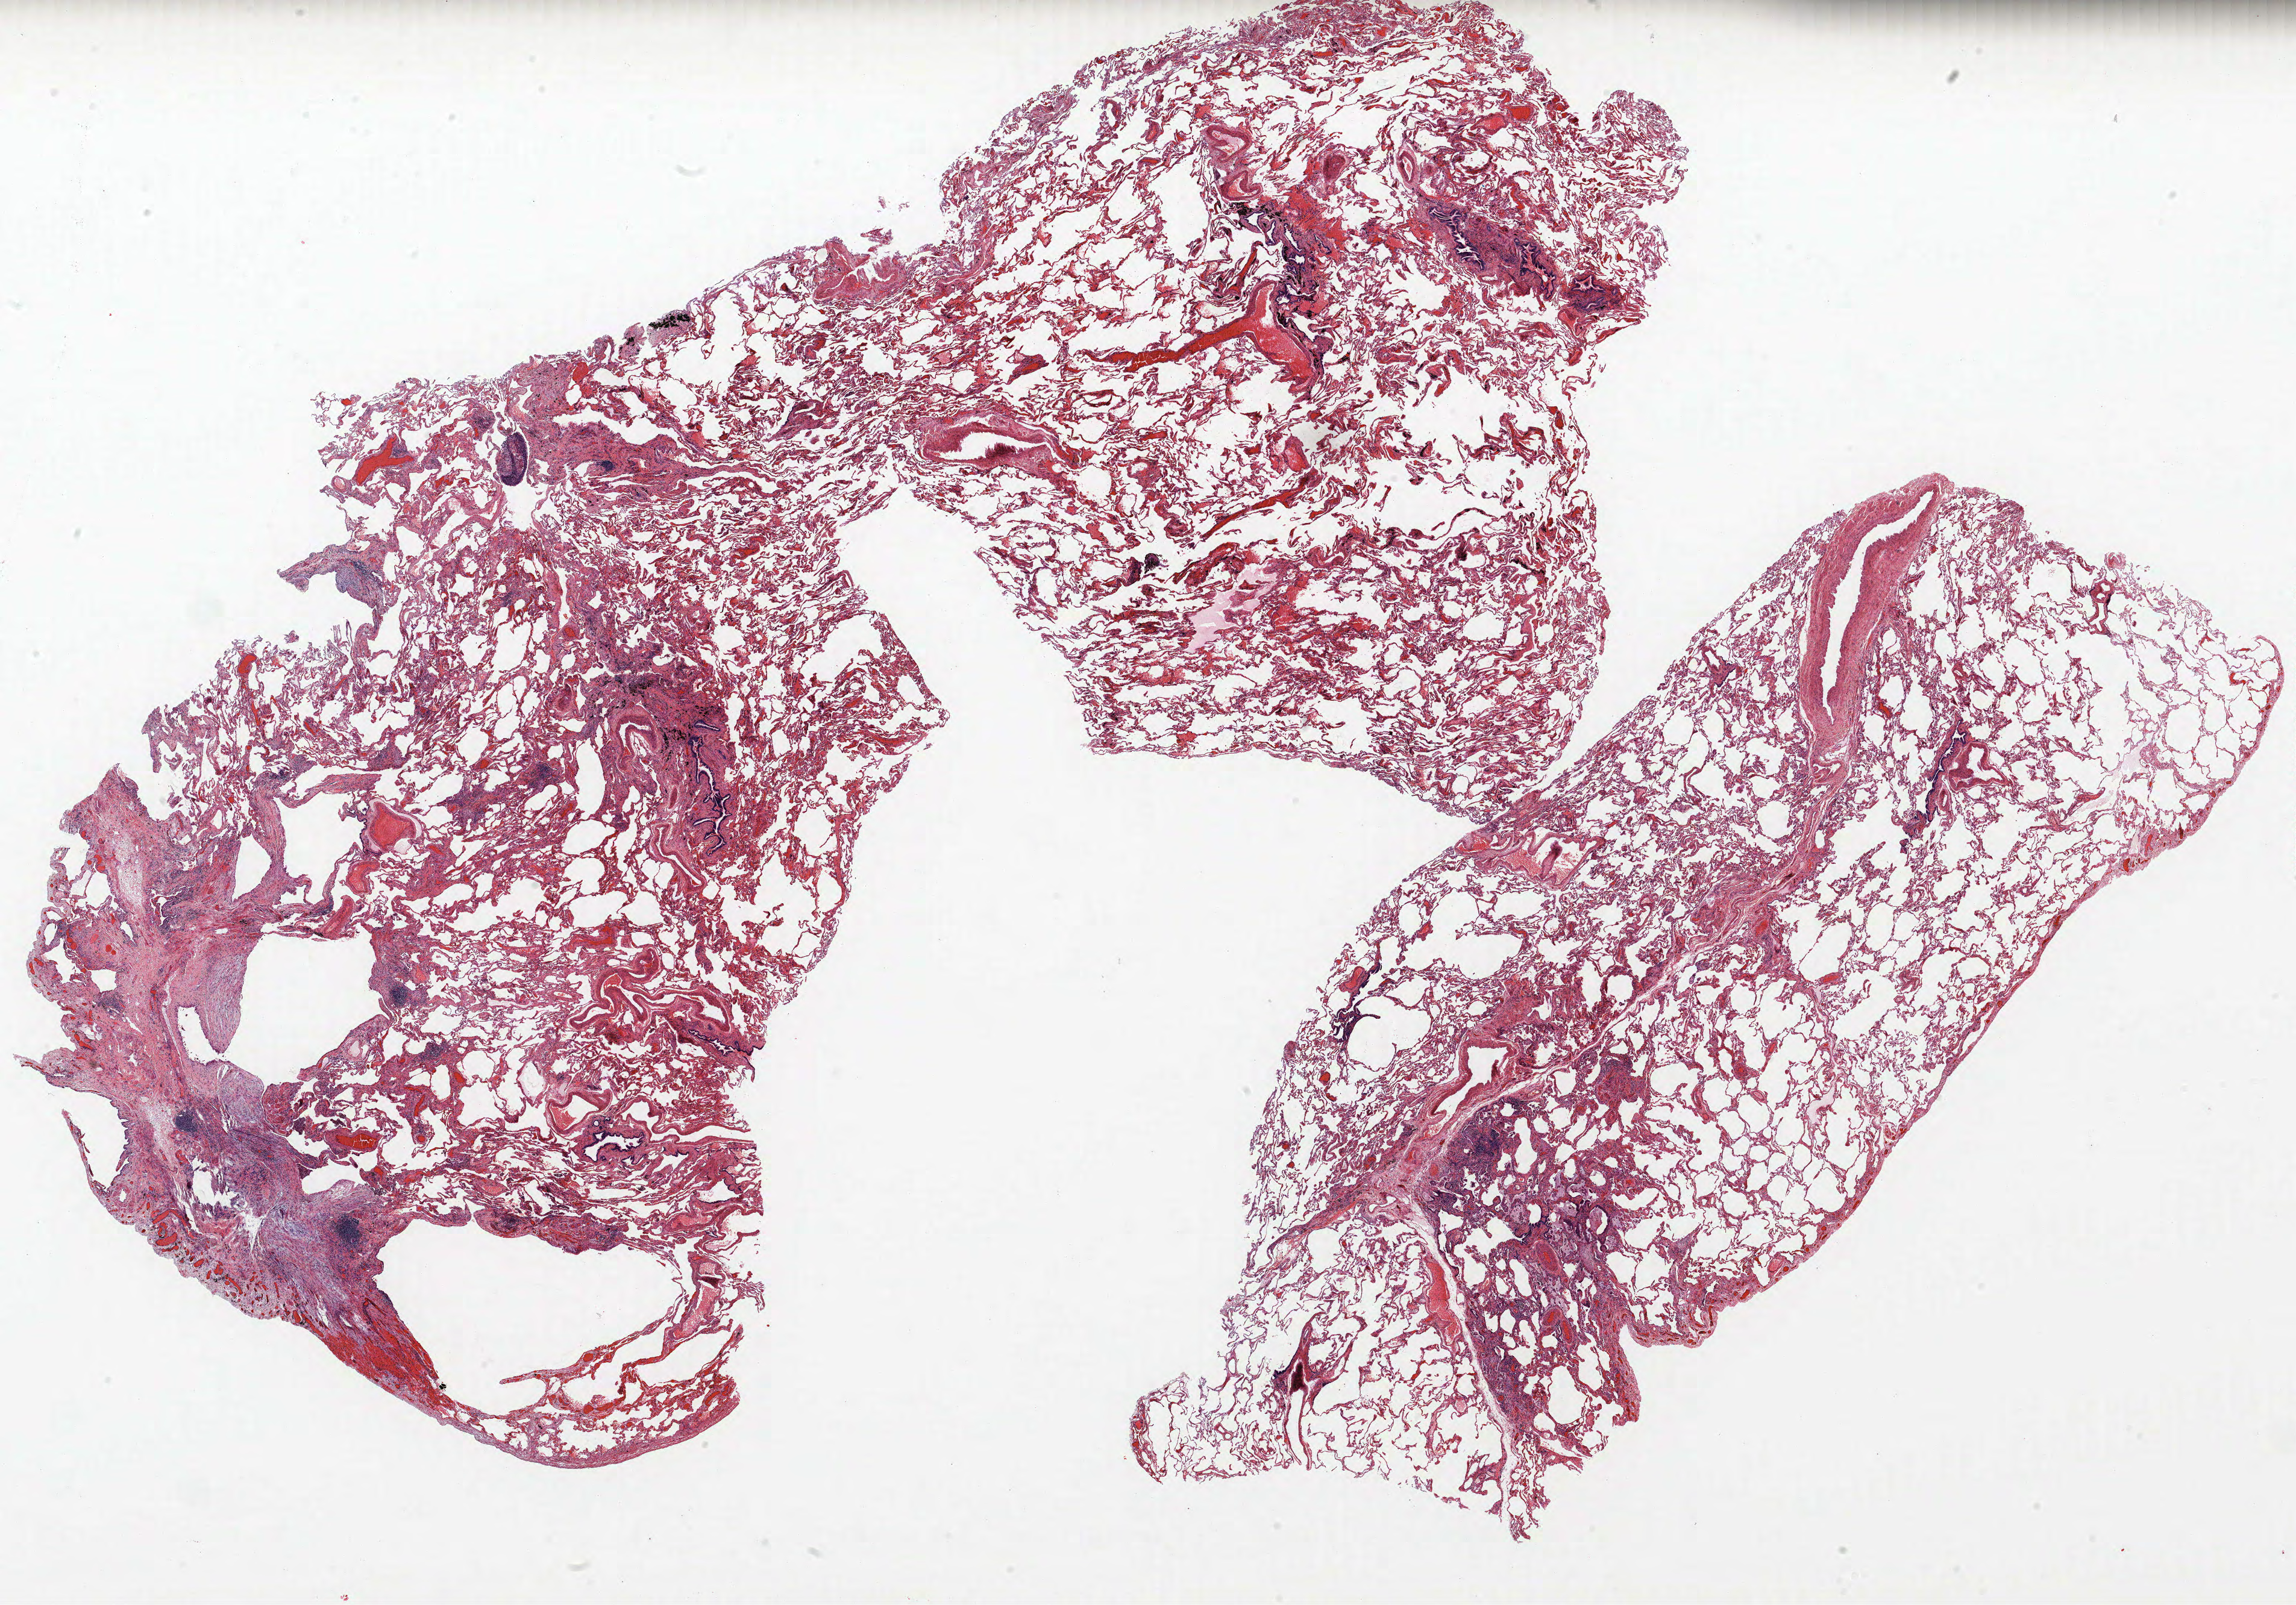
Whole-slide histology image, H&E-stained — a low-resolution overview of the entire scanned area, about 30.5 x 21.3 mm; FFPE section; lung. Male, age 65 at enrolment. Former smoker at enrolment.
Primary tumour location (clinical record): left upper lobe. Tumour size (pathology): 20 mm. Participant's lung-cancer diagnosis: Squamous cell carcinoma, NOS. Stage (AJCC 6th edition): IB.